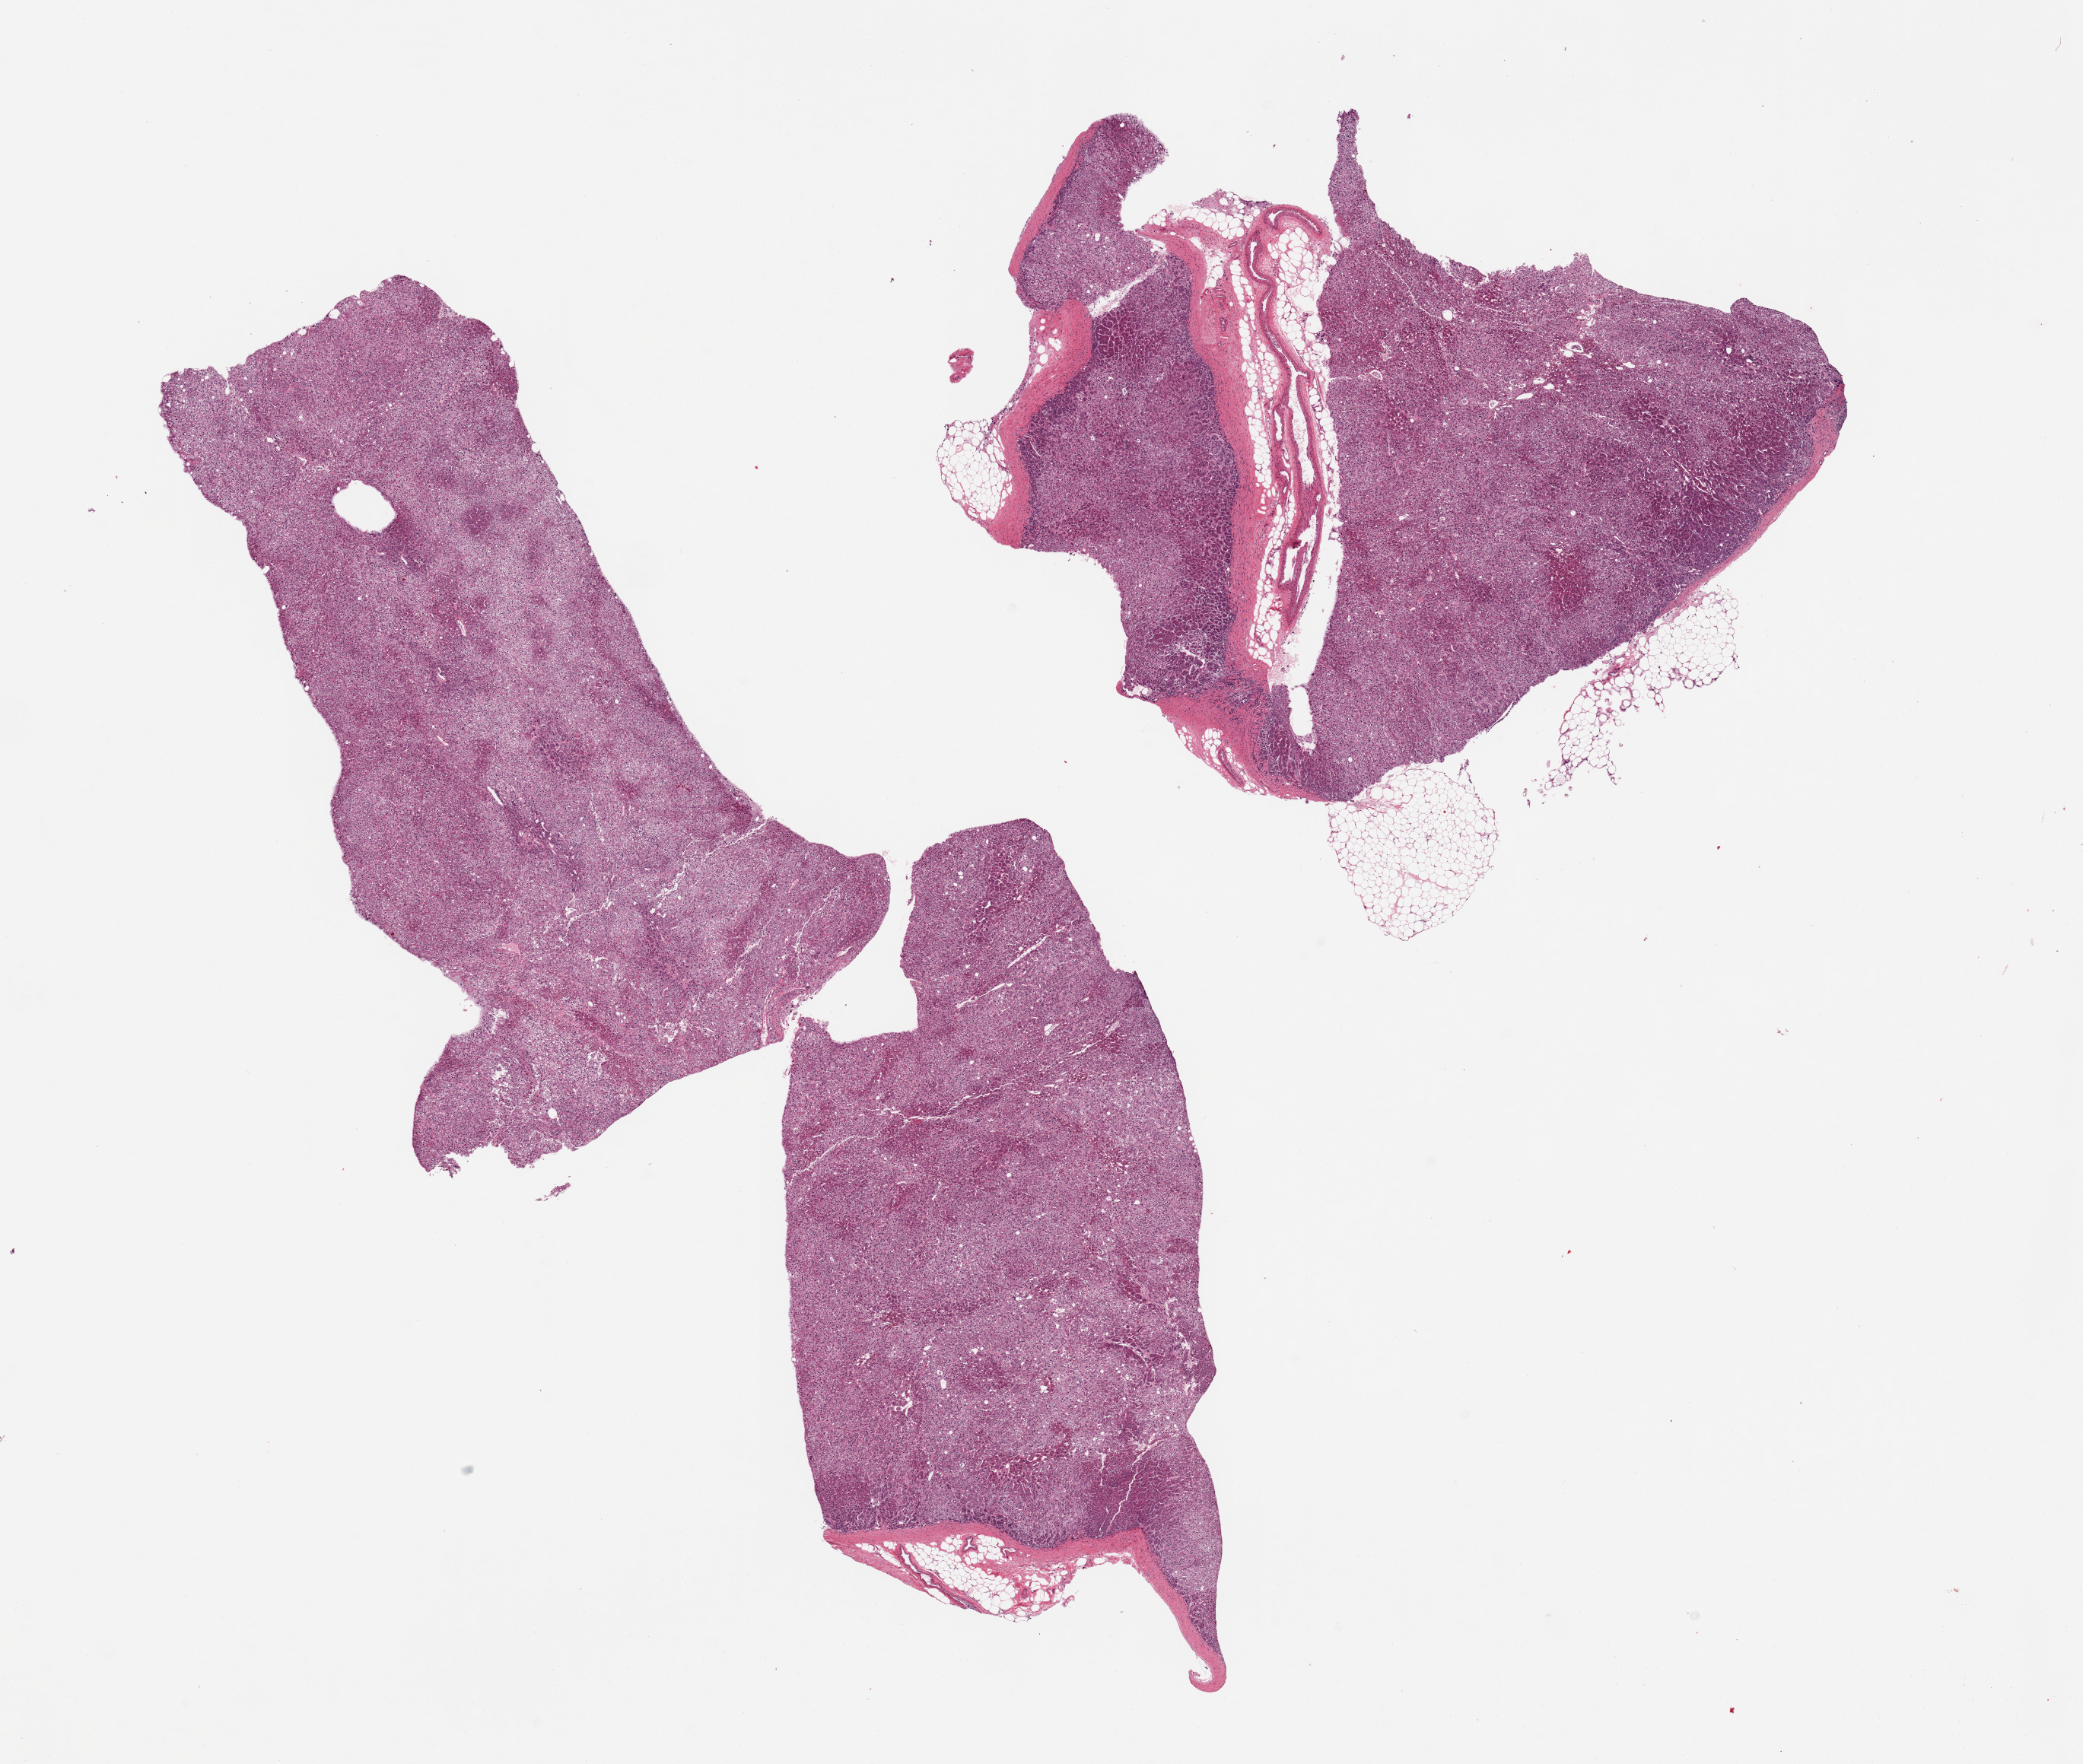
H&E whole-slide image — a low-resolution overview of the entire scanned area, about 21.7 x 18.3 mm (from a 20x scan); PAXgene-fixed, paraffin-embedded tissue; section of adrenal gland (target tissue); tissue donor sample. Female donor.
Reviewer comment on this tissue sample: 3 pieces.